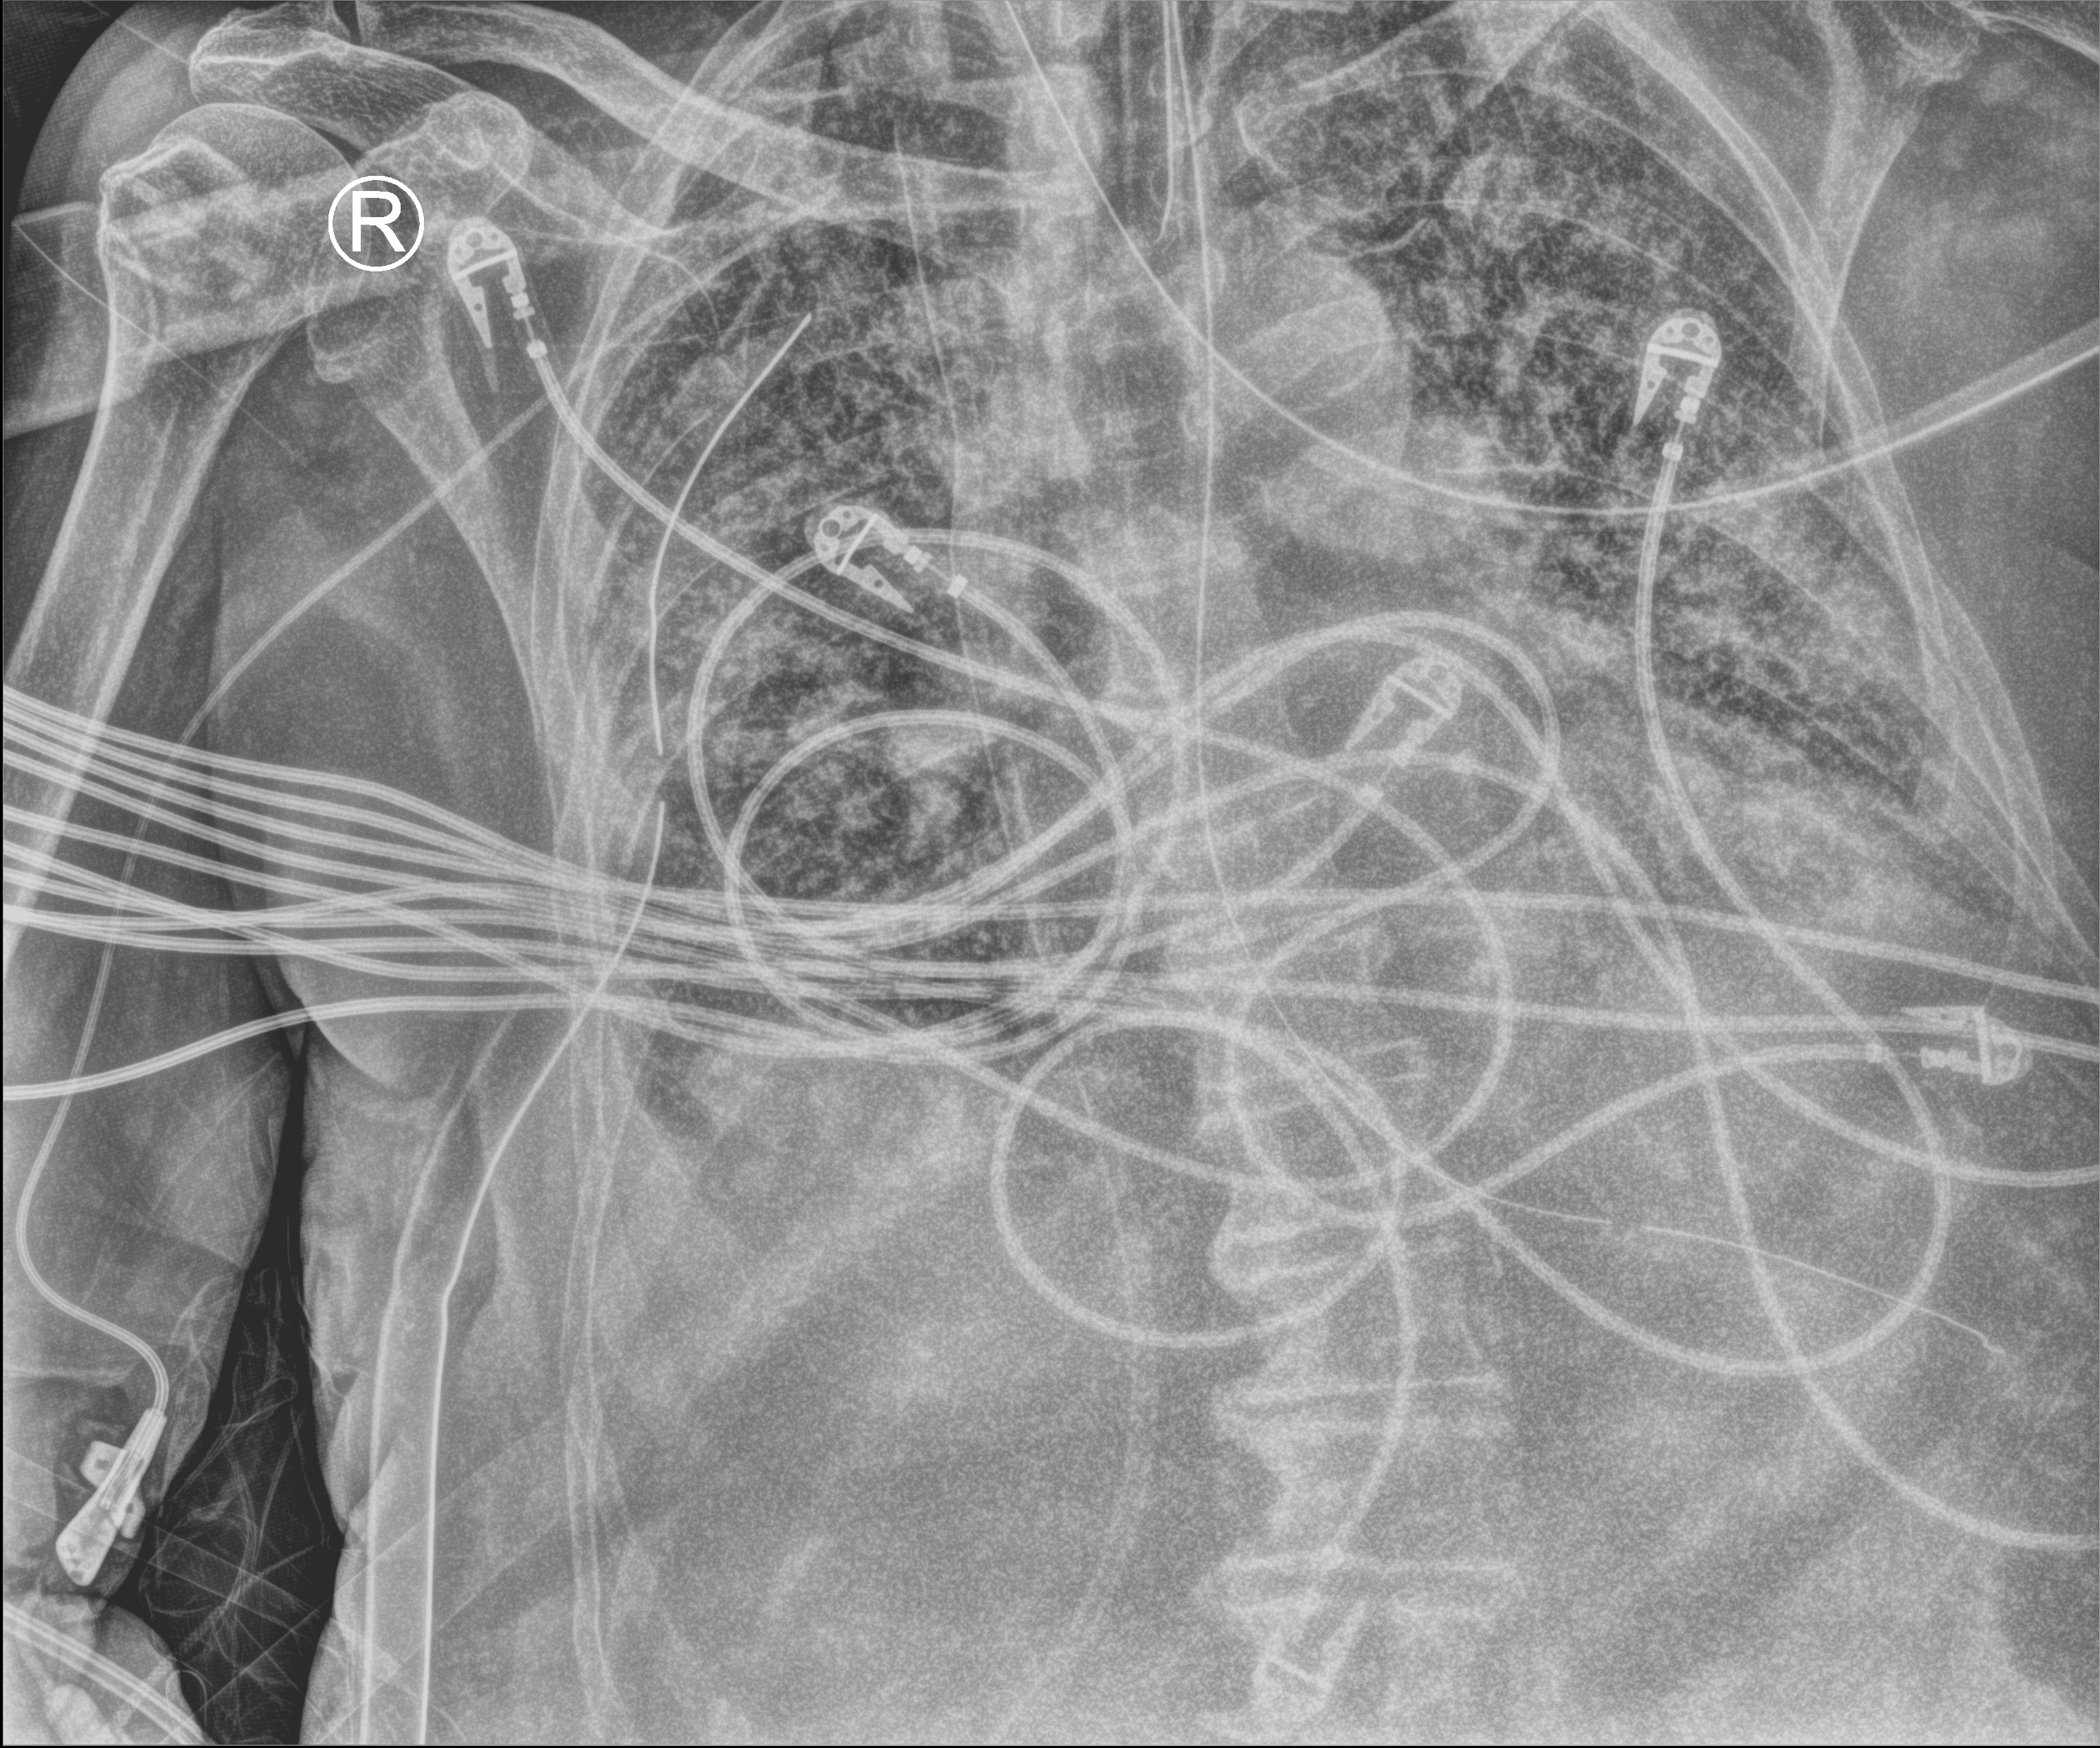
Bedside chest radiograph (computed radiography), anteroposterior (AP) projection. Male patient hospitalised with COVID-19, age 75–90 years.
From the hospital-stay record, not from the radiograph (when in the stay this image was taken is not recorded): mechanically ventilated during this hospital stay: yes.